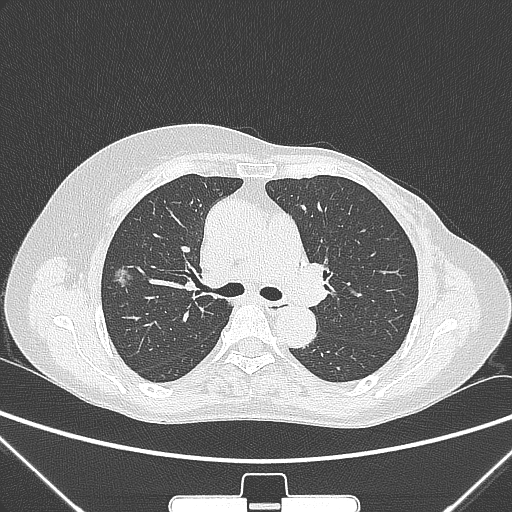
Chest CT, one axial slice. Slice 161 of 265 in the series (ordered by position). 120 kVp. Lung window (W 1500 / L -600 HU). 512 × 512 image matrix, field of view 350 × 350 mm. Female patient, age 64 years. Case-level facts recorded for this patient, not image findings: clinical TNM (as recorded): T1c N0 M0.
Annotated regions visible in this slice (bounding box drawn by a radiologist):
- lung tumour (recorded histology: adenocarcinoma): bounding box <105,258,139,301> (left, top, right, bottom; pixels)